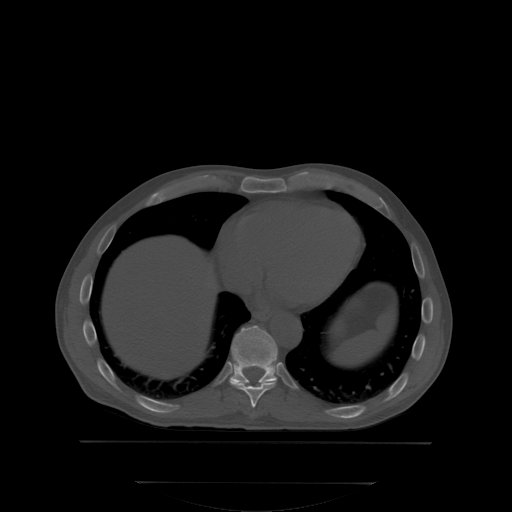
CT including the spine, one axial slice. Slice 200 of 350 in the series (ordered by position). Bone window (W 1800 / L 400 HU). 2.5 mm slice thickness. 512 × 512 image matrix, field of view 500 × 500 mm. Patient: male, 58 years. Case-level facts recorded for this patient, not image findings: primary cancer: prostate.
Structures marked on this image (semi-automatically segmented with operator editing):
- T10 vertebra: bounding box (x1, y1, x2, y2) in pixels: (230, 326, 278, 383)
- T9 vertebra: (230, 382, 276, 408)